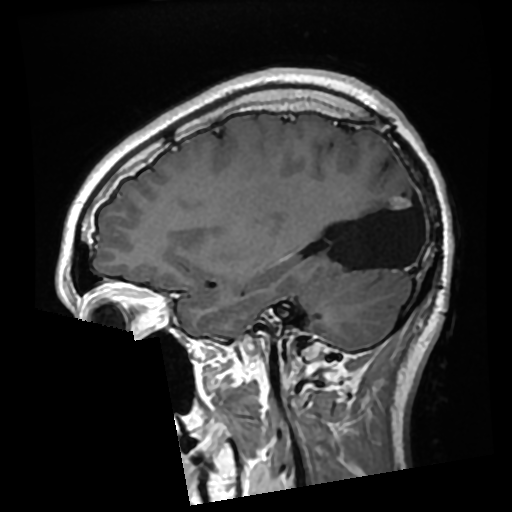
Brain MRI from a brain-tumour surgery series, one sagittal slice; slice 96 of 276 in the series (ordered by position); T1-weighted post-contrast; 0.7 mm slice thickness; 512 × 512 image matrix. From the clinical record (not read from this slice): histopathology: Glioma with ependymal features; WHO grade: 2; tumour location: Left Parietal.
Structures marked on this image (manually delineated by an expert):
- previous resection cavity: bounding box (x1, y1, x2, y2) in pixels: (325, 182, 417, 270)
- tumour: (392, 196, 411, 210)